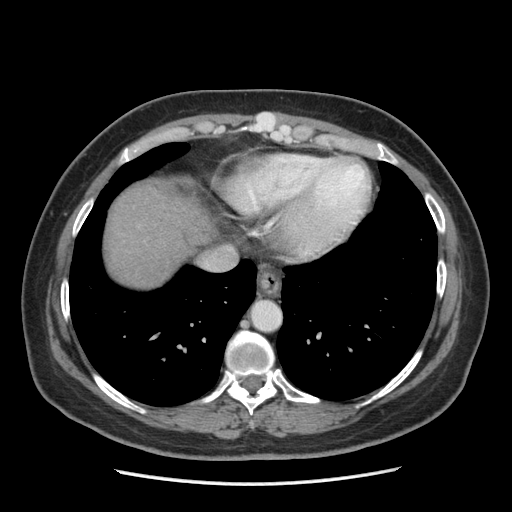
Contrast-enhanced abdominal CT (liver protocol), one axial slice. Position 173 of 185 along the scan axis. Reconstruction kernel STANDARD. Soft-tissue window (W 400 / L 40 HU). 2.5 mm slice thickness. 512 × 512 image matrix, field of view 360 × 360 mm. Case-level facts recorded for this patient, not image findings: diagnosis: hepatocellular carcinoma (patient treated with transarterial chemoembolisation; whether this scan precedes or follows treatment is not stated here); TNM stage (as recorded): Stage-I; Child-Pugh class: A; tumour differentiation: poorly differentiated; tumour nodularity: uninodular.
Structures marked on this image (semi-automatically segmented with operator editing):
- liver parenchyma outside the tumour (the mass and vessels are separate outlines, so this box may not span the whole liver): bounding box (x1, y1, x2, y2) in pixels: (106, 184, 218, 288)